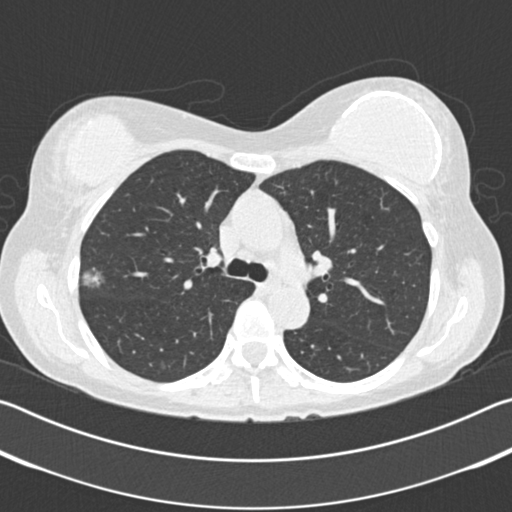
Low-dose screening chest CT, axial slice. Second screening round (one year after baseline). Lung window (W 1500 / L -600 HU). 2 mm slice thickness. Slice 60 of 183 in the series. Female, age 58 years at enrolment. Former smoker at enrolment.
• Expert reader's lesion annotation, bounding box <66,257,120,306> (left, top, right, bottom; pixels).
• Reader record for this screening exam (exam-level; its link to the box is not recorded): non-calcified nodule or mass ≥4 mm, right upper lobe, 15 × 13 mm, poorly defined margins, ground glass attenuation, pre-existing on the prior screen: no.
• Official screen result: positive, change unspecified: nodule(s) >= 4 mm or enlarging nodule(s), mass(es), or other non-specific abnormalities suspicious for lung cancer.